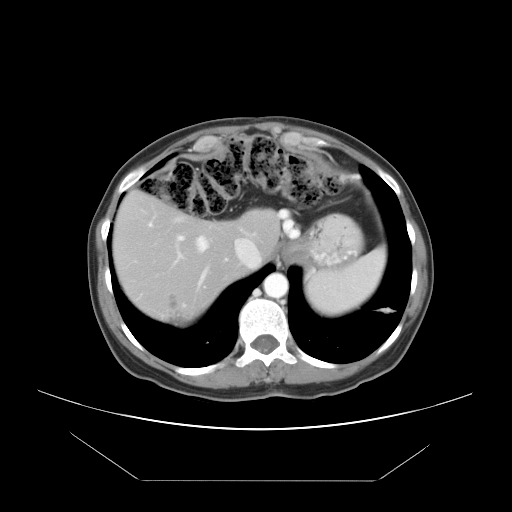
Contrast-enhanced abdominal CT, one axial slice; position 36 of 45 along the scan axis; 120 kVp; intravenous contrast given; soft-tissue window (W 400 / L 40 HU); 5 mm slice thickness; 512 × 512 image matrix, field of view 405 × 405 mm. Female patient, age 52 years. Case-level facts recorded for this patient, not image findings: diagnosis: colorectal cancer liver metastases, imaged before liver resection; multiple liver metastases: yes; largest metastasis: 2.5 cm; disease in both lobes: no.
Annotated regions visible in this slice (expert manual segmentation):
- hepatic veins: bounding box [x1, y1, x2, y2] px = [174, 217, 210, 290]
- liver: [116, 190, 278, 324]
- planned liver remnant (the part of the liver to remain after resection): [116, 190, 278, 300]
- portal vein (with intrahepatic branches): [149, 222, 227, 263]
- liver metastasis: [166, 296, 187, 323]